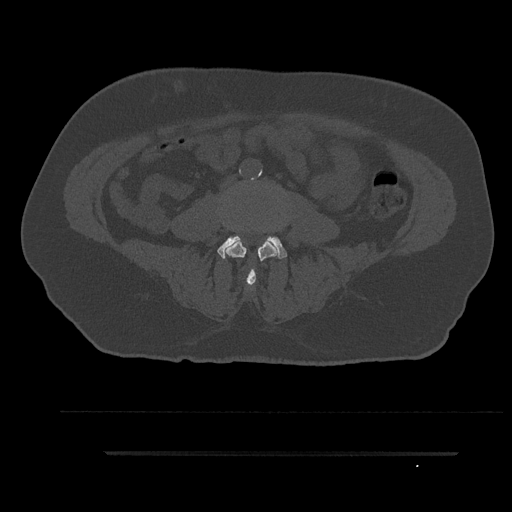
CT including the spine, one axial slice. Position 8 of 797 along the scan axis. Reconstruction kernel Br40s/3. Bone window (W 1800 / L 400 HU). 0.5 mm slice thickness. 512 × 512 image matrix. Male patient, age 63 years. From the clinical record (not read from this slice): primary cancer: renal.
Structures marked on this image (semi-automatically segmented with operator editing):
- L3 vertebra: bounding box <225,238,277,285> (left, top, right, bottom; pixels)
- L4 vertebra: <217,236,287,259>